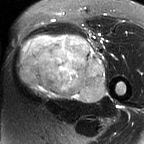
MRI of an extremity soft-tissue mass, one axial slice; position 37 of 60 along the scan axis; T2-weighted fat-saturated; MR volume resampled by the dataset authors to the PET/CT grid (not the native acquisition matrix); 144 × 144 image matrix, field of view 141 × 141 mm. Female patient. From the clinical record (not read from this slice): histological type: pleiomorphic leiomyosarcoma; grade: intermediate; site of the primary tumour: left thigh.
Structures marked on this image (expert contour drawn on MRI and transferred to this co-registered scan by the dataset authors):
- gross tumour volume including surrounding oedema: box from (x=18, y=33) to (x=105, y=102) px
- gross tumour volume (mass): (x=18, y=35)–(x=105, y=102)